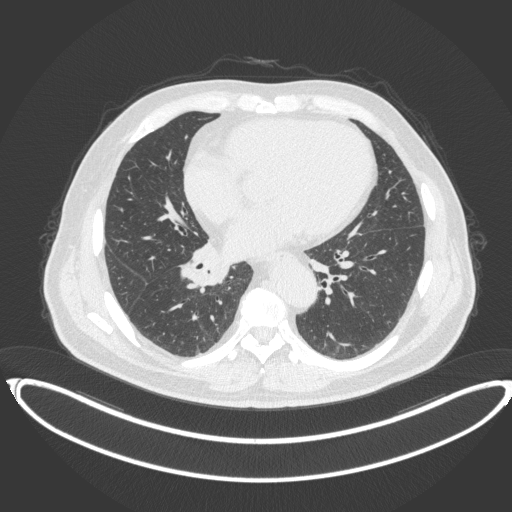
Chest CT, one axial slice. Position 174 of 383 along the scan axis. Reconstruction kernel B31f. Lung window (W 1500 / L -600 HU). 1 mm slice thickness. 512 × 512 image matrix, field of view 448 × 448 mm. Male patient, age 61 years. From the clinical record (not read from this slice): clinical TNM (as recorded): T1b N1 M0.
Structures marked on this image (bounding box drawn by a radiologist):
- lung tumour (recorded histology: squamous cell carcinoma): box from (x=177, y=238) to (x=233, y=295) px